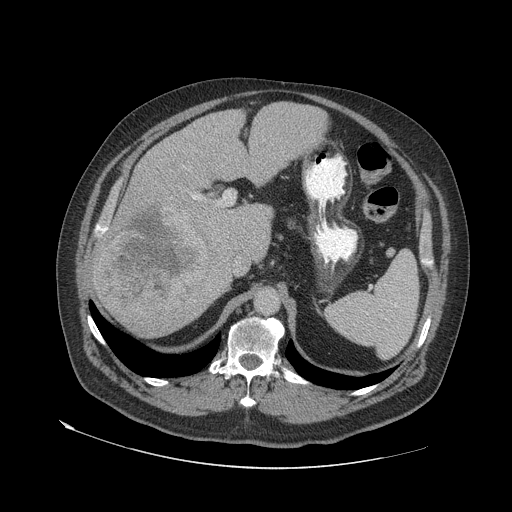
Contrast-enhanced abdominal CT (liver protocol), one axial slice. Reconstruction kernel STANDARD. 140 kVp. Soft-tissue window (W 400 / L 40 HU). 512 × 512 image matrix. Case-level facts recorded for this patient, not image findings: diagnosis: hepatocellular carcinoma (patient treated with transarterial chemoembolisation; whether this scan precedes or follows treatment is not stated here); TNM stage (as recorded): Stage-IVA; Child-Pugh class: A; tumour differentiation: well differentiated; tumour nodularity: multinodular.
Annotated regions visible in this slice (semi-automatically segmented with operator editing):
- liver parenchyma outside the tumour (the mass and vessels are separate outlines, so this box may not span the whole liver): box from (x=92, y=102) to (x=326, y=336) px
- mass: (x=95, y=204)–(x=212, y=319)
- liver vessels: (x=96, y=194)–(x=221, y=234)